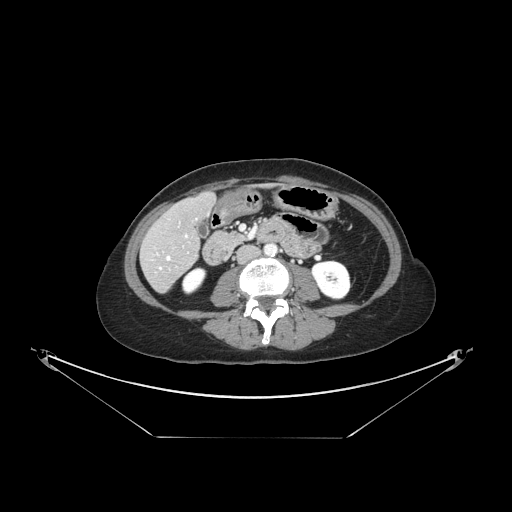
Contrast-enhanced abdominal CT, one axial slice; slice 44 of 148 in the series (ordered by position); reconstruction kernel STANDARD; 120 kVp; intravenous contrast given; soft-tissue window (W 400 / L 40 HU); 2.5 mm slice thickness; 512 × 512 image matrix, field of view 500 × 500 mm. Female patient, age 73 years. From the clinical record (not read from this slice): diagnosis: colorectal cancer liver metastases, imaged before liver resection; multiple liver metastases: no; largest metastasis: 1 cm.
Annotated regions visible in this slice (expert manual segmentation):
- hepatic veins: bounding box <157,235,187,269> (left, top, right, bottom; pixels)
- liver: <143,195,215,291>
- planned liver remnant (the part of the liver to remain after resection): <161,195,215,242>